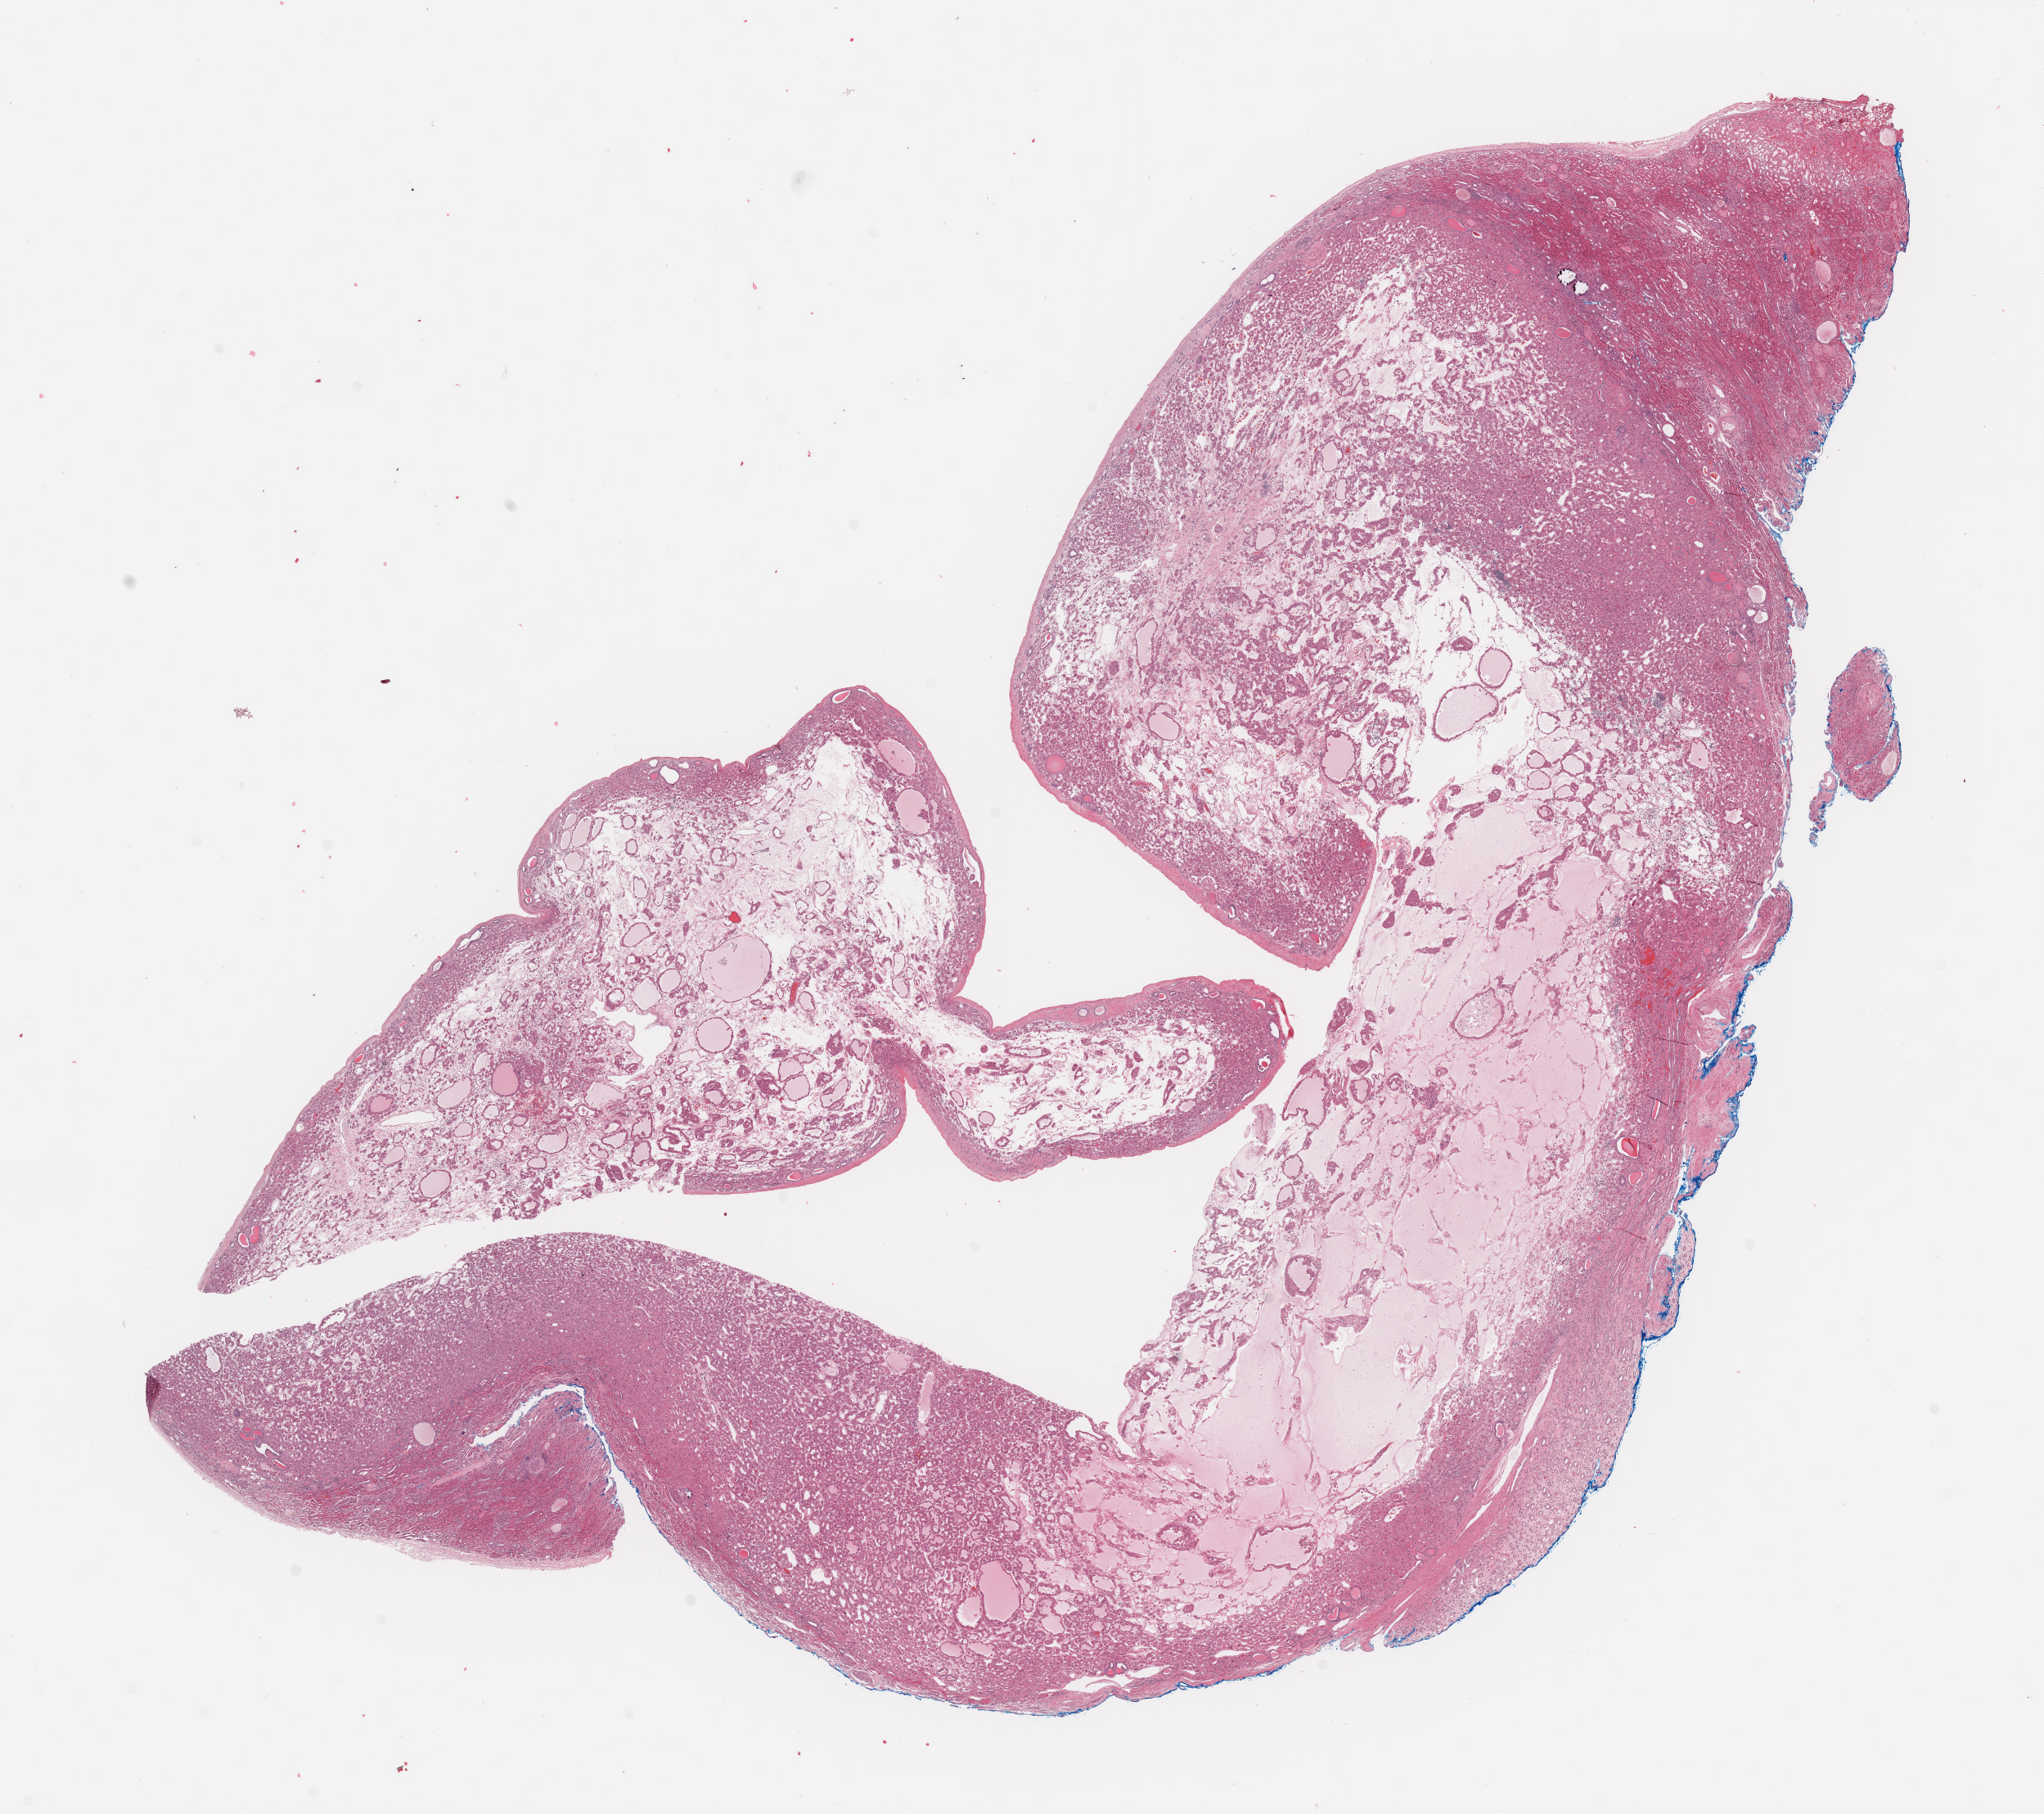
H&E whole-slide image — whole scanned area (about 19.8 x 17.5 mm) shown as a low-resolution overview; formalin-fixed paraffin-embedded (FFPE) diagnostic section; primary tumour sample from the kidney. Male patient; age at initial diagnosis 75 years.
Histologic diagnosis: Renal cell carcinoma, chromophobe type.